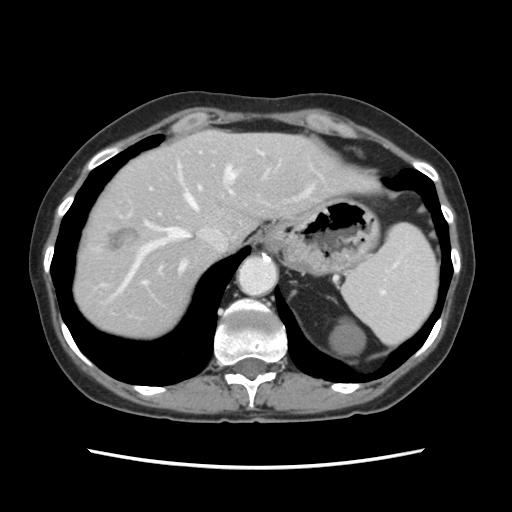
Contrast-enhanced abdominal CT, one axial slice. Position 96 of 120 along the scan axis. Intravenous contrast given. Soft-tissue window (W 400 / L 40 HU). 512 × 512 image matrix, field of view 330 × 330 mm. Female patient, age 70 years. From the clinical record (not read from this slice): diagnosis: colorectal cancer liver metastases, imaged before liver resection; multiple liver metastases: no; largest metastasis: 2.5 cm.
Outlined on this slice (outlined manually by an expert reader):
- hepatic veins: bounding box (x1, y1, x2, y2) in pixels: (113, 166, 236, 296)
- liver: (74, 131, 365, 339)
- planned liver remnant (the part of the liver to remain after resection): (139, 131, 364, 272)
- portal vein (with intrahepatic branches): (143, 151, 263, 284)
- liver metastasis: (109, 228, 139, 251)